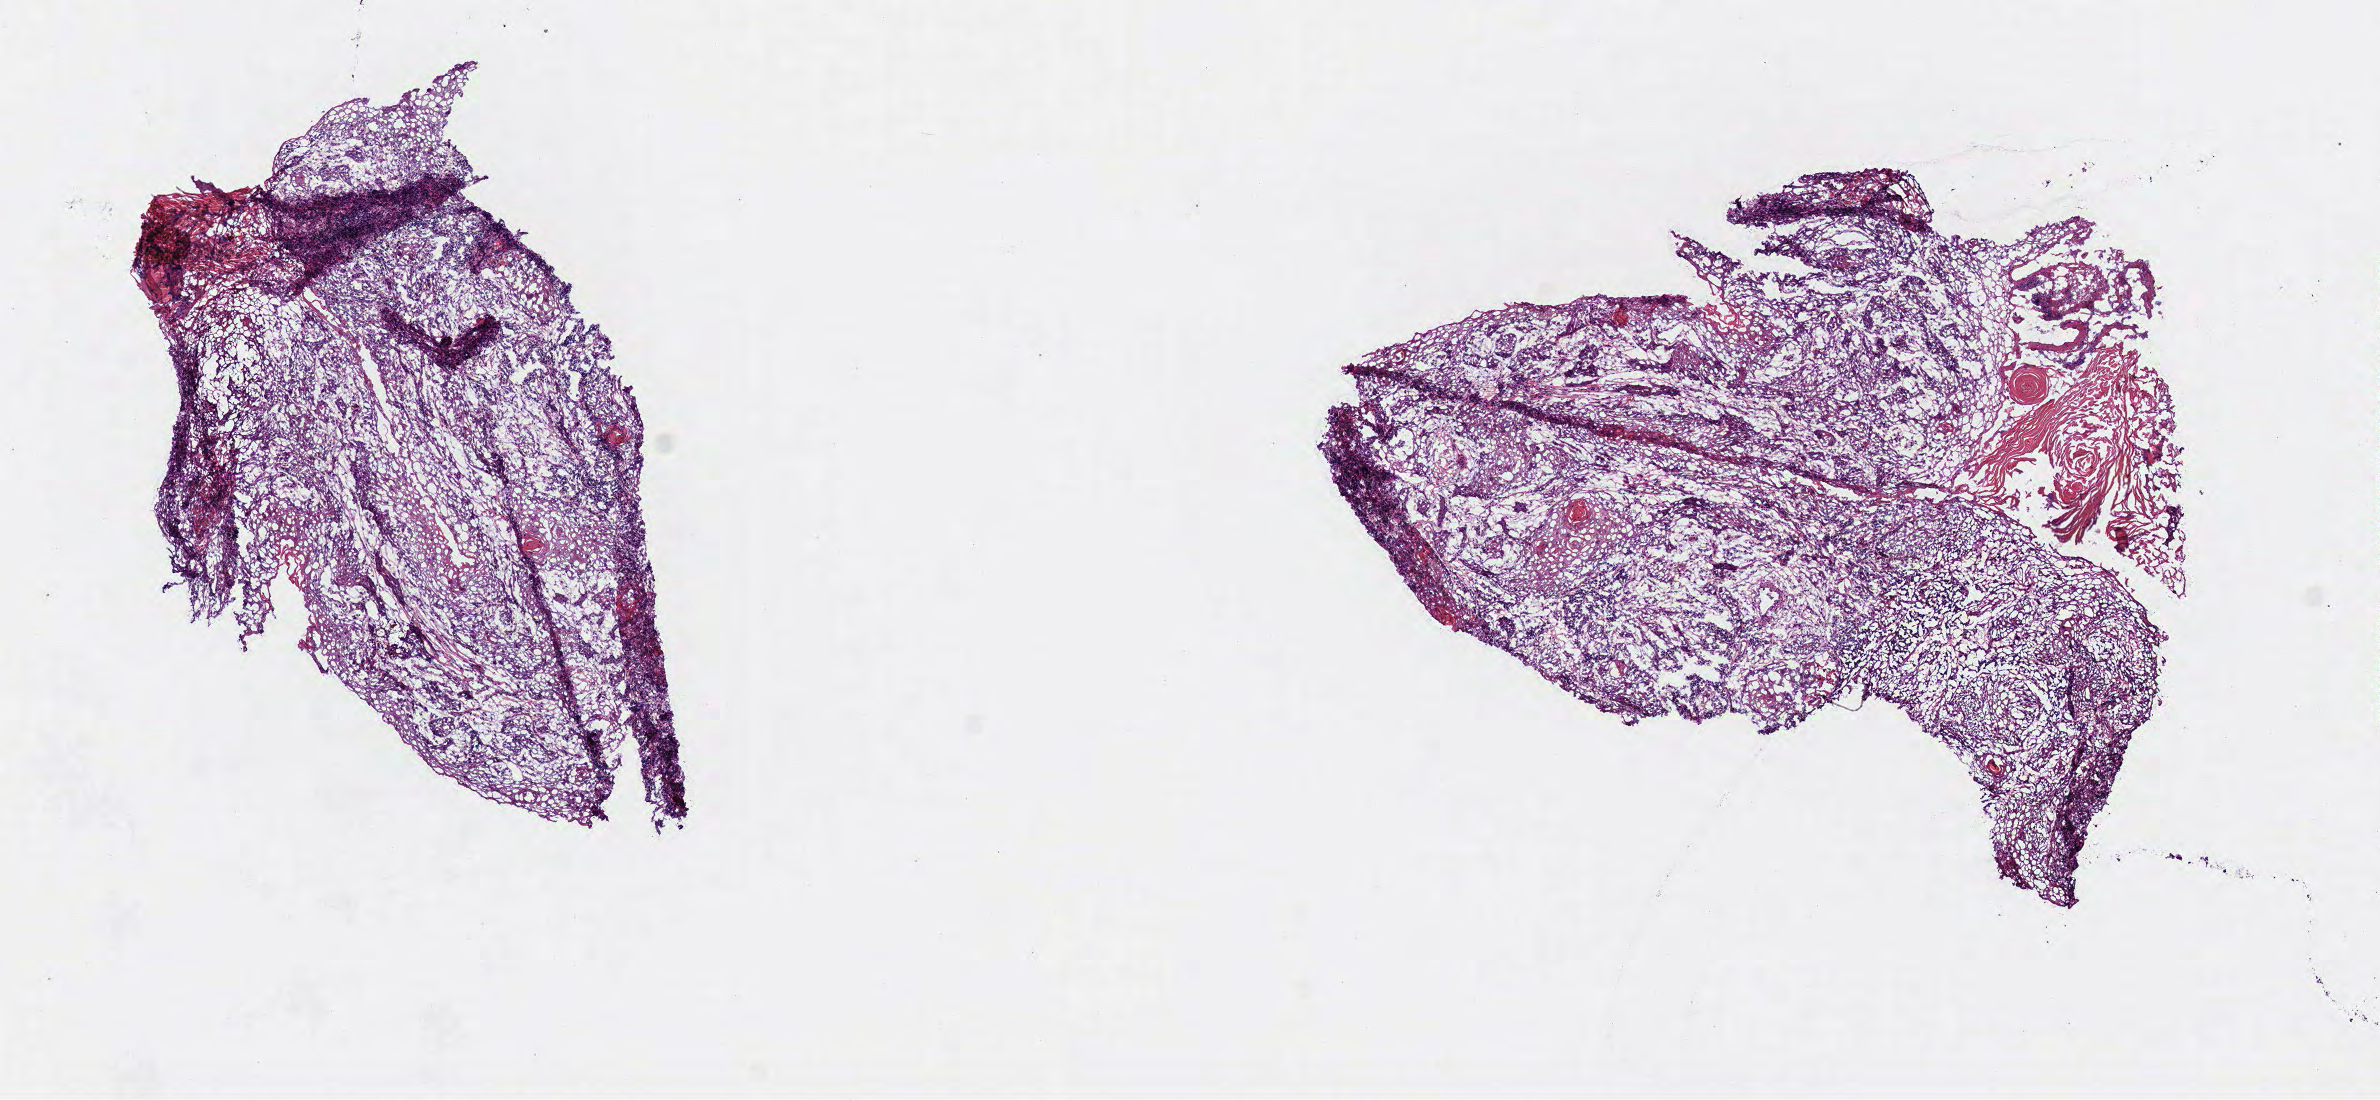
Digitized H&E tissue section (whole slide) — a low-resolution overview of the entire scanned area, about 9.4 x 4.3 mm, frozen section from the bottom of the tissue portion, sample: primary tumour, head and neck. Male patient; age at initial diagnosis 59 years. Histologic grade: G2 (moderately differentiated). Pathologist review of this section (percent, as recorded): tumour cells 90%, tumour nuclei 80%, normal cells 0%, stromal cells 10%, necrosis 0%.
- lymph nodes positive (case pathology): 11 of 50 examined
- AJCC pathologic stage: IVA
- diagnosis: Squamous cell carcinoma, NOS (tongue, NOS)
- TNM: T4a N2b